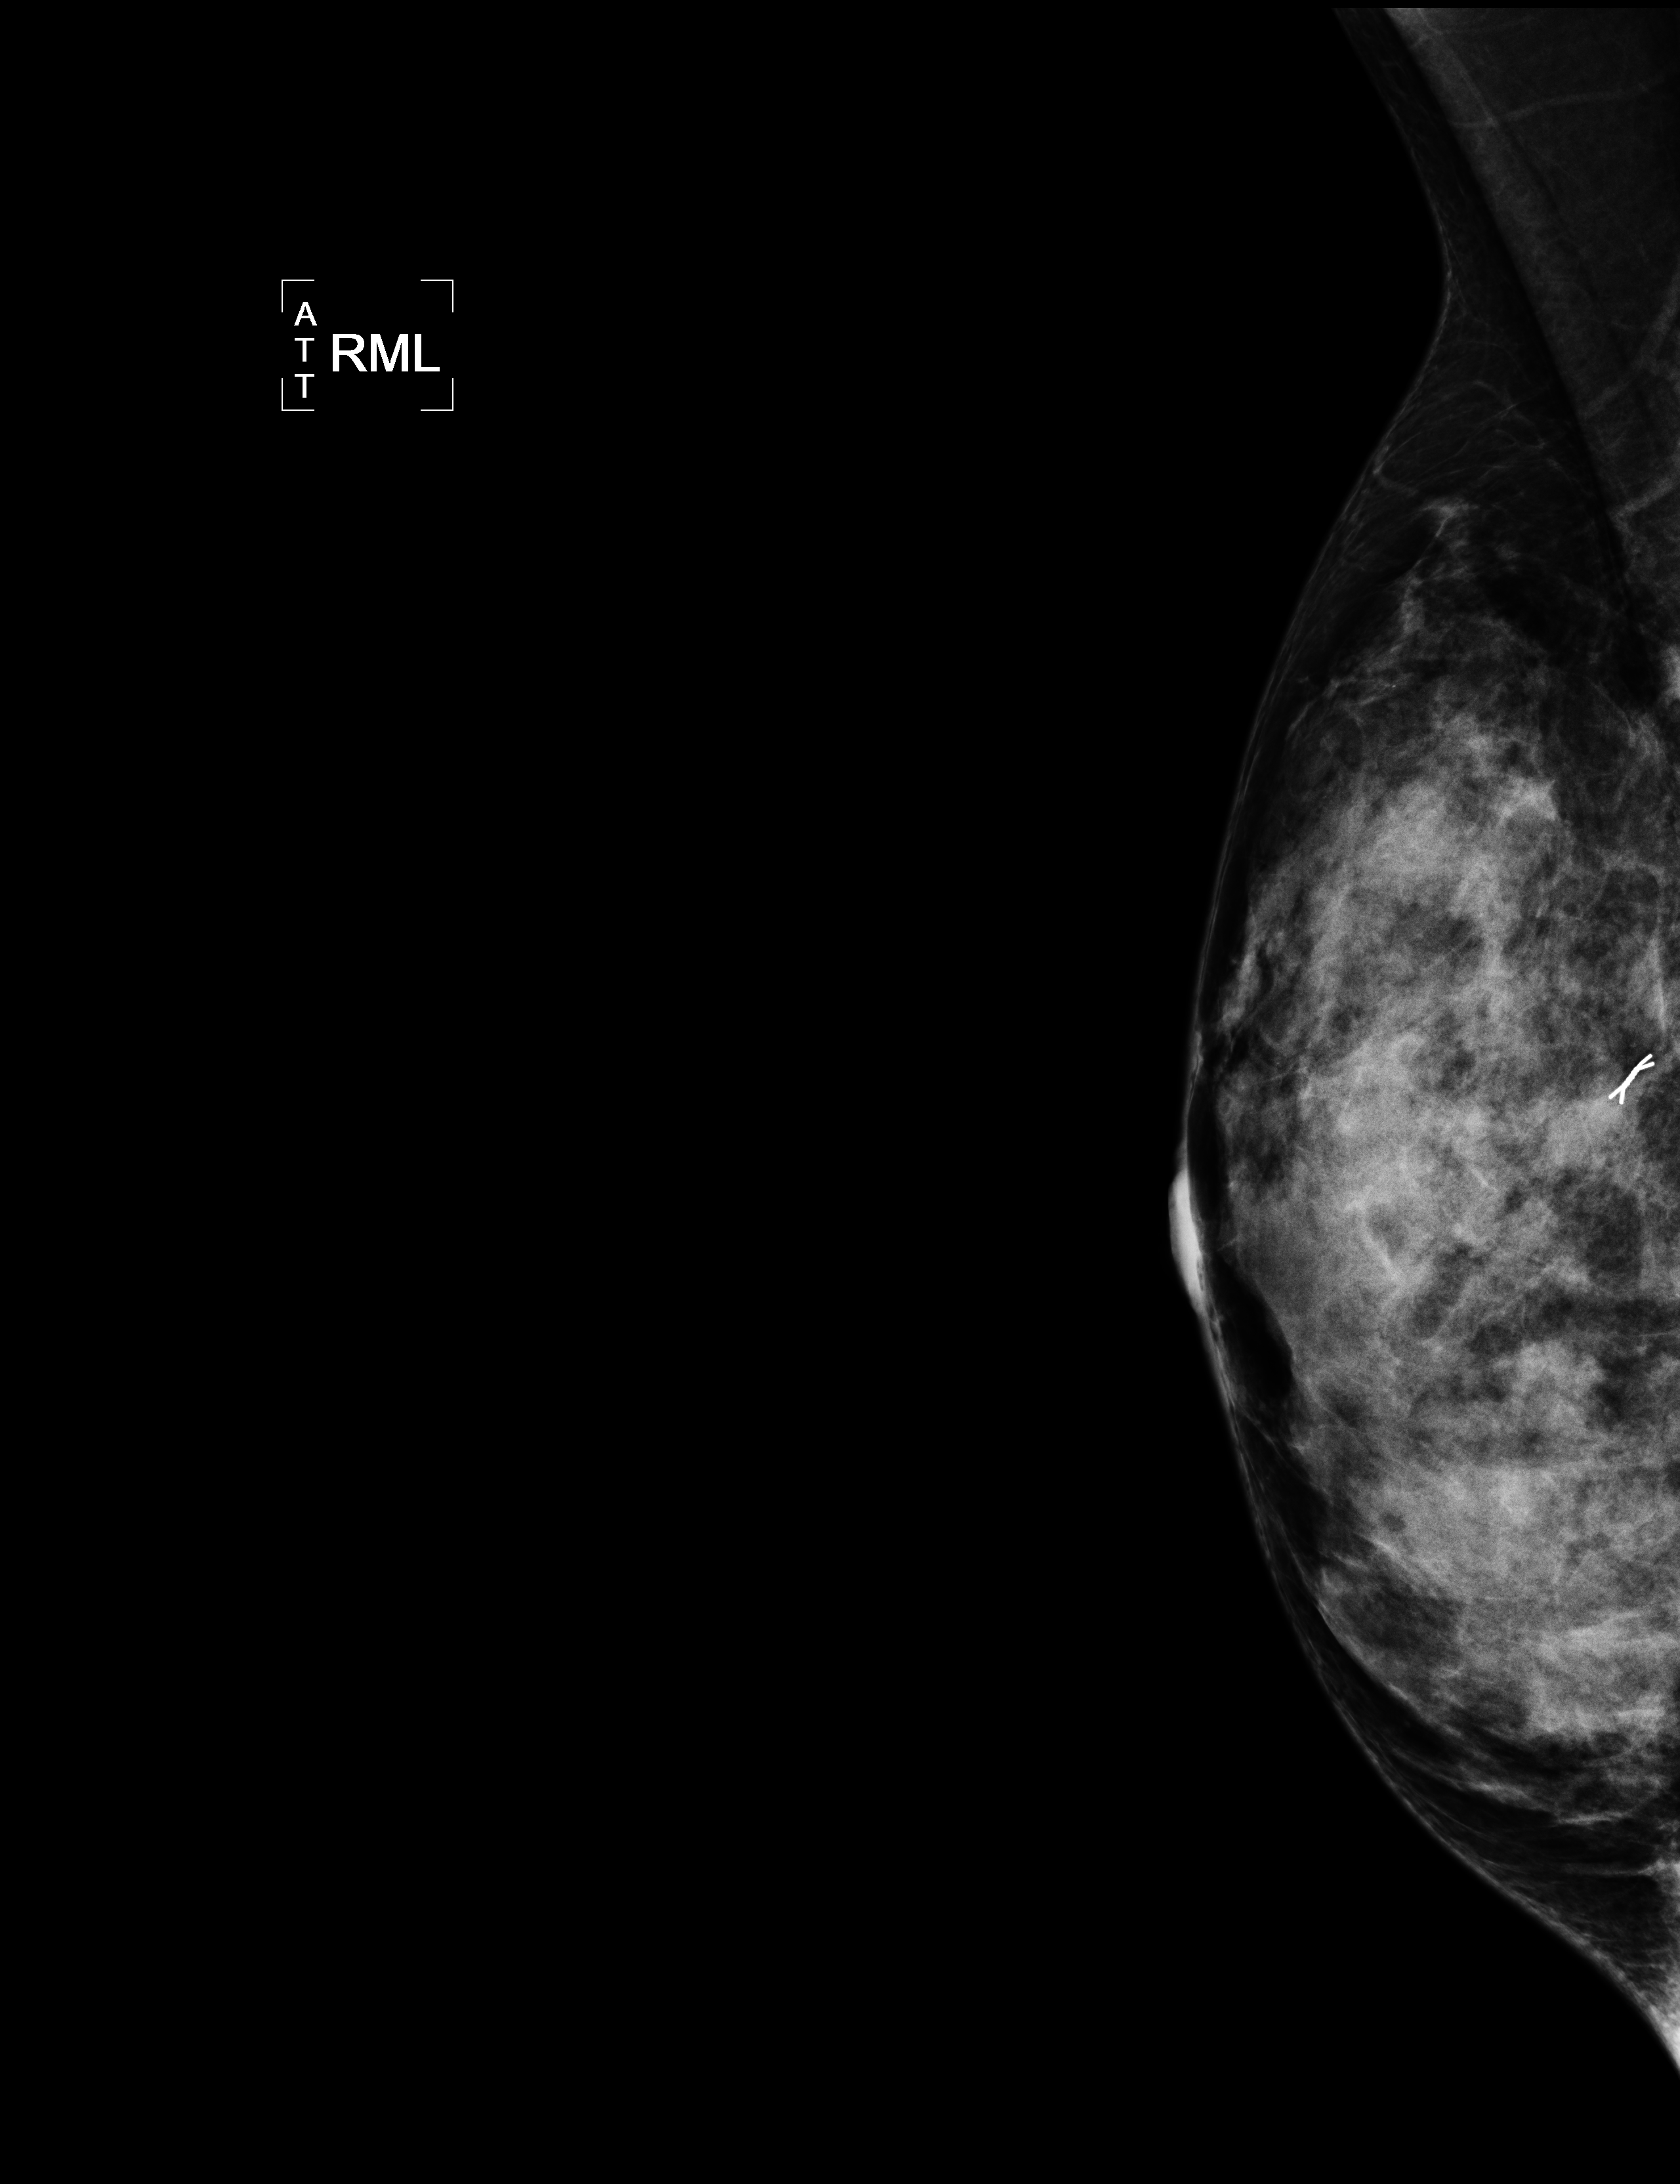
Mammogram, right breast, ML view.
Pathology recorded for this patient (not read from this image): pathology diagnosis: Invasive ductal carcinoma, modified Scarff-Bloom-Richardson grade II/III. No intraductal carcinoma component seen. (right breast); receptor status (as recorded): ER pos (strong), PR pos (strong), HER2 neg (weak).